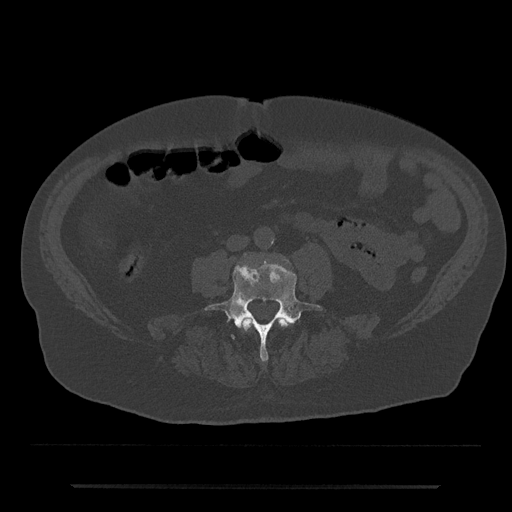
CT including the spine, one axial slice; slice 360 of 797 in the series (ordered by position); reconstruction kernel Br40s/3; 120 kVp; bone window (W 1800 / L 400 HU); 512 × 512 image matrix. Male patient, age 80 years. From the clinical record (not read from this slice): primary cancer: prostate.
Outlined on this slice (semi-automatically segmented with operator editing):
- L3 vertebra: box from (x=240, y=318) to (x=291, y=330) px
- L4 vertebra: (x=205, y=254)–(x=322, y=361)